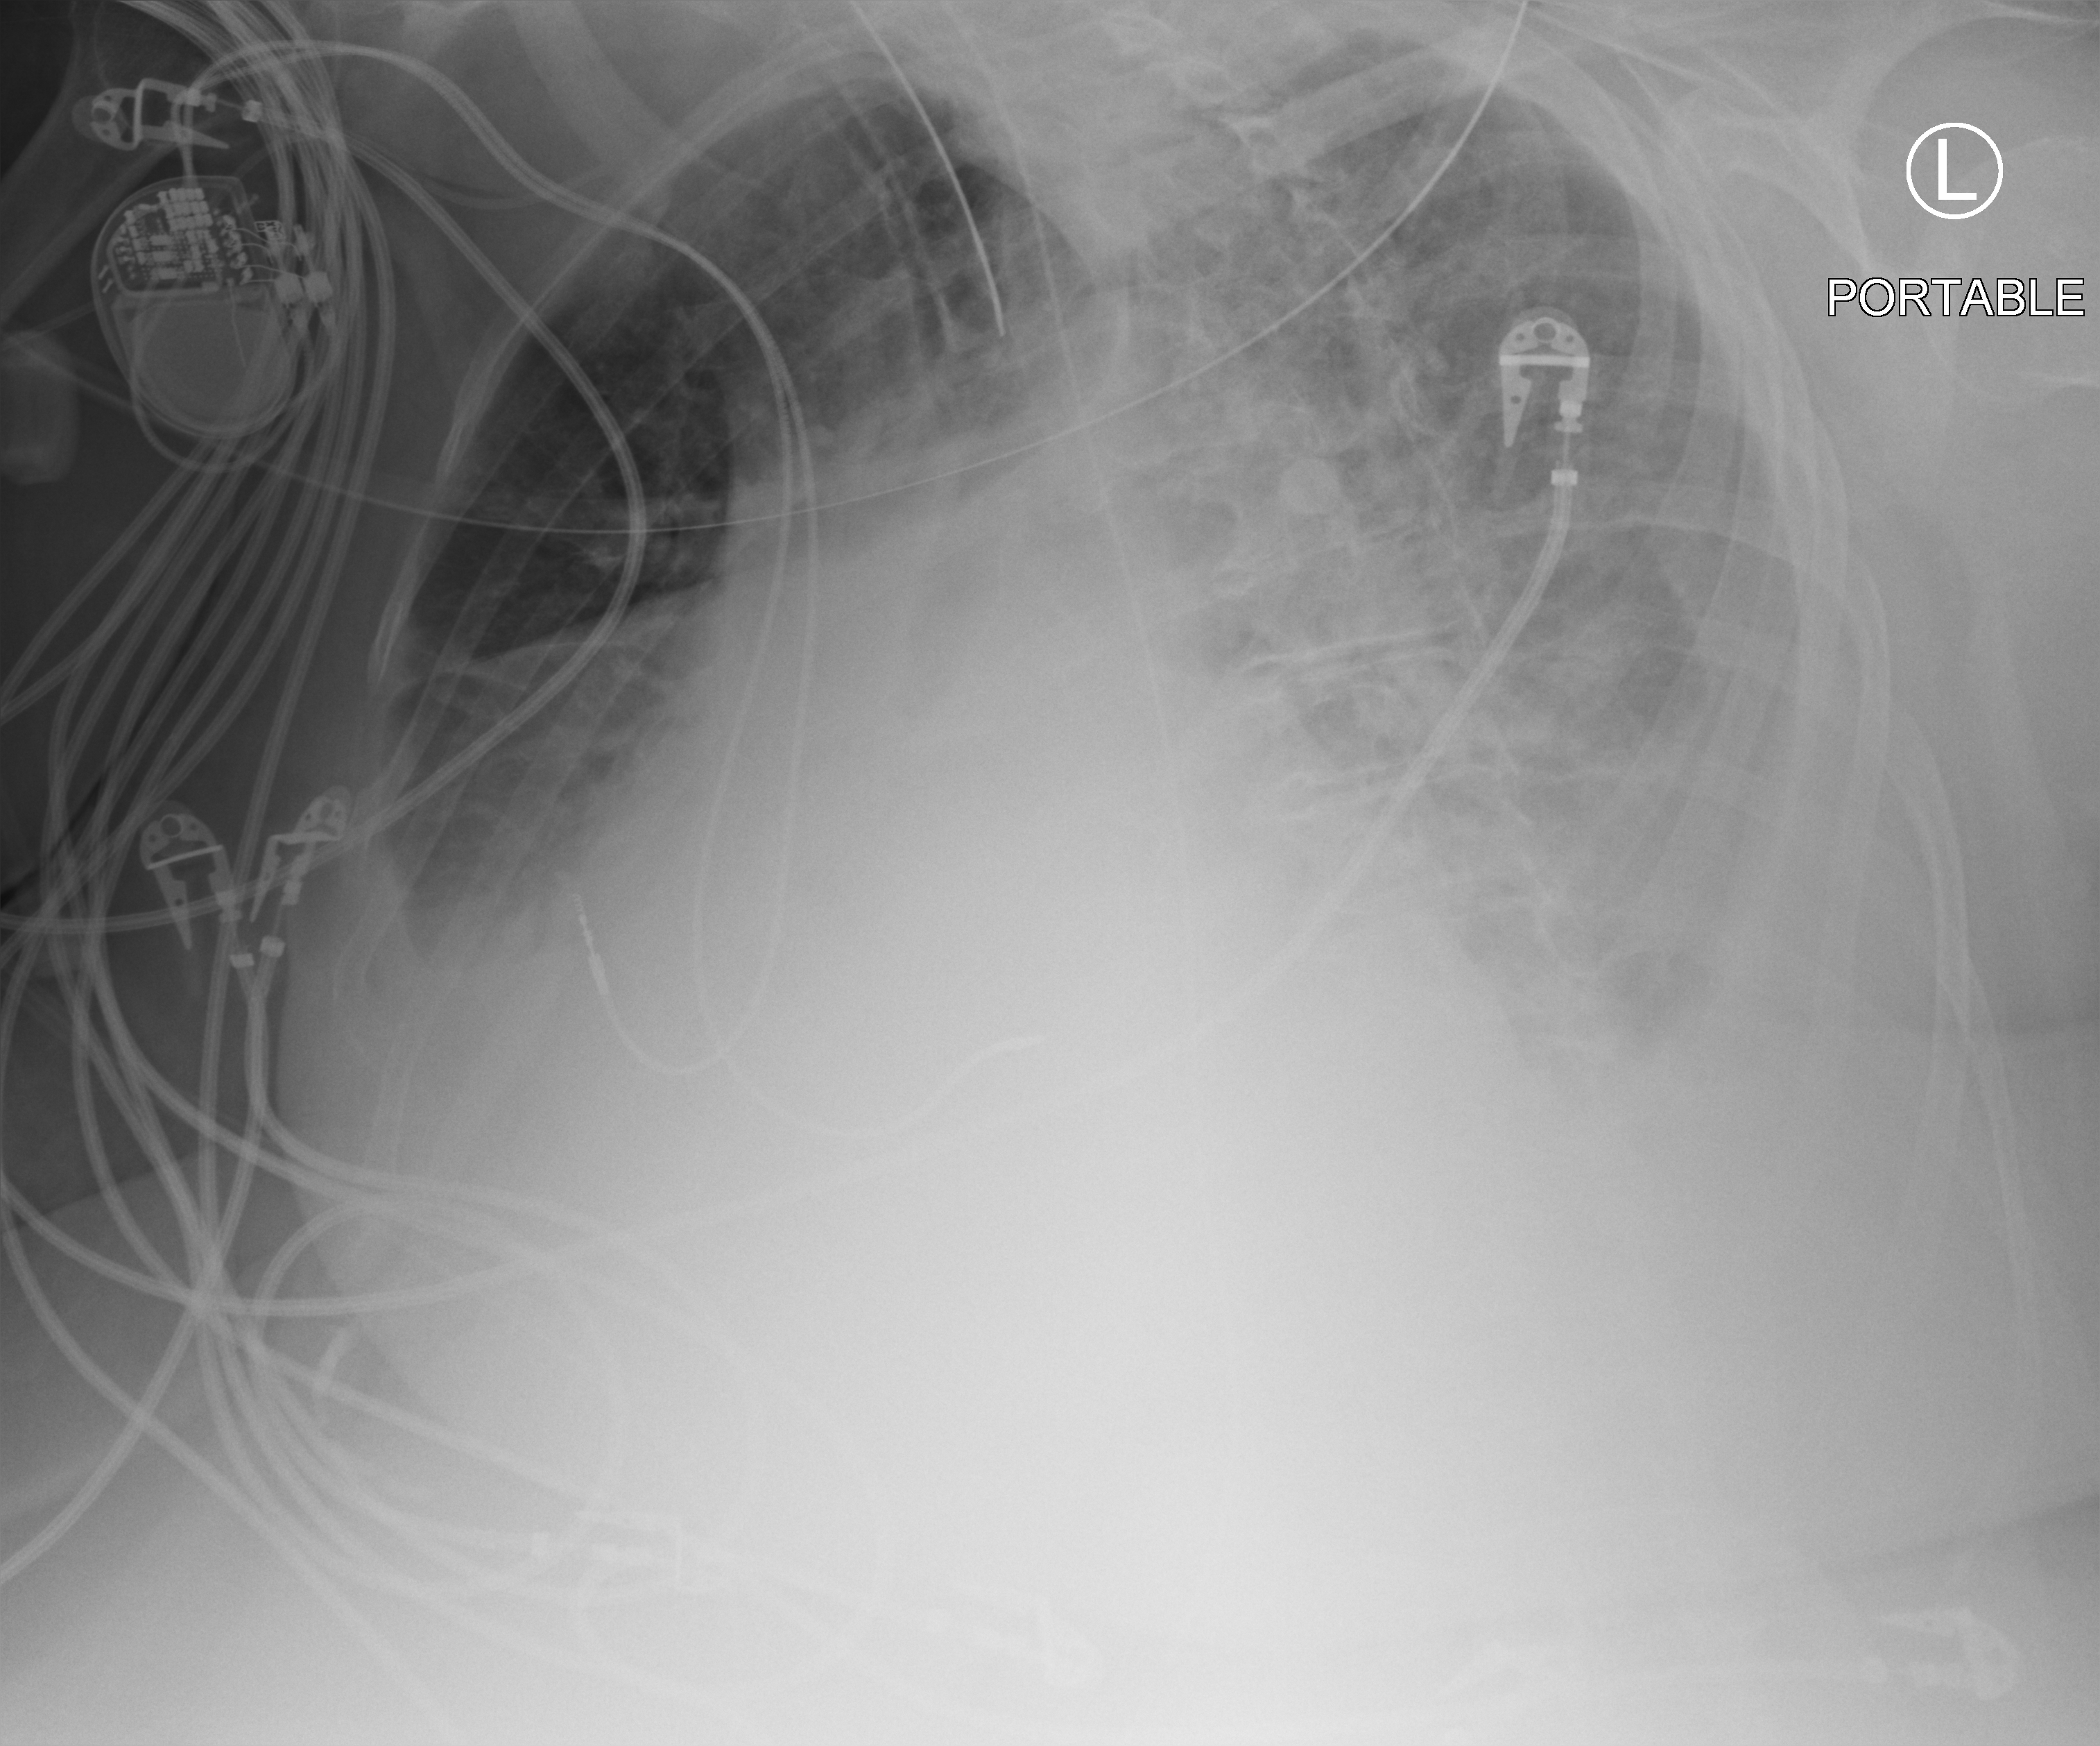
Portable chest radiograph. Female patient hospitalised with COVID-19, age 75–90 years.
From the hospital-stay record, not from the radiograph (when in the stay this image was taken is not recorded):
- smoking status (admission record): former
- mechanically ventilated during this hospital stay: yes
- chronic kidney disease (admission record): yes